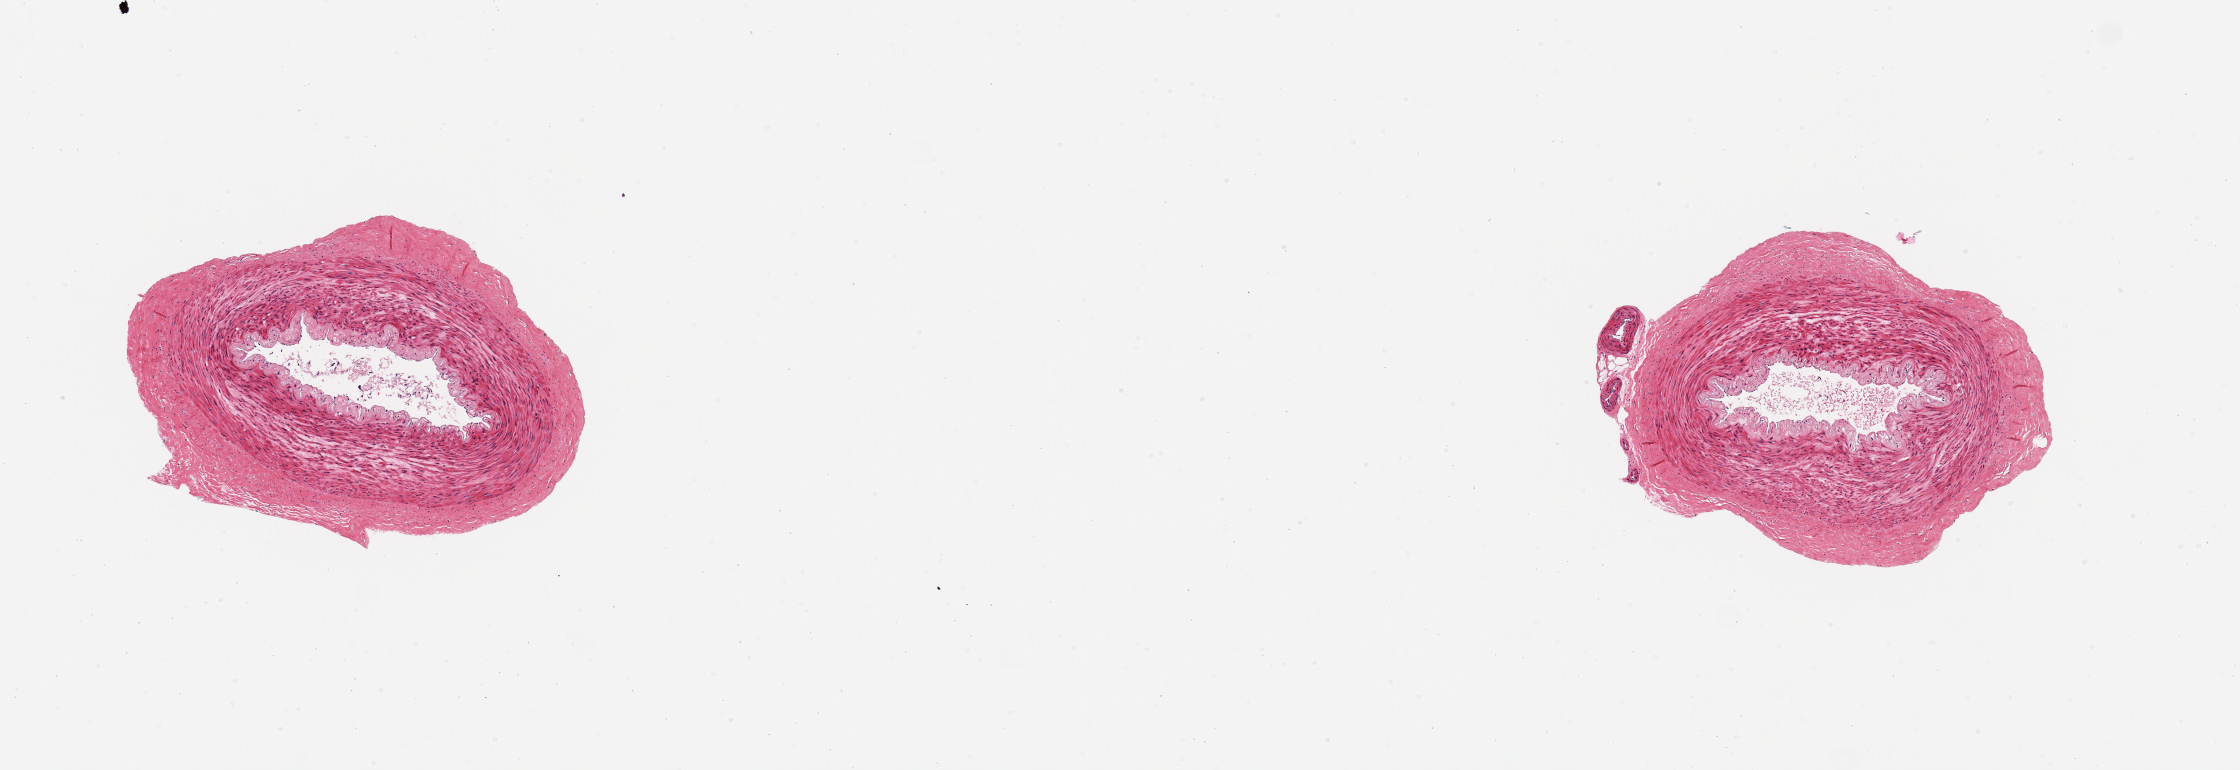
Whole-slide image, H&E stain, brightfield, low-resolution overview of the scanned area, about 8.9 x 3.0 mm; PAXgene-fixed paraffin-embedded (PFPE) section; section of tibial artery (target tissue); tissue donor sample. Female donor.
Reviewer comment on this tissue sample: 2 aliquots, ~1.5mm d.